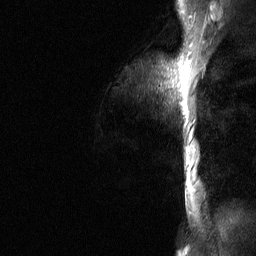
Breast MRI (dynamic contrast-enhanced), one sagittal slice; dynamic contrast-enhanced study with each time point stored as its own series, time point 2 of 3 at this slice position (early post-contrast, ordered by acquisition time); 1.5 T; TE 4.8 ms, TR 27 ms; 2 mm slice thickness; 256 × 256 image matrix, field of view 200 × 200 mm. Patient: female, 36 years. From the clinical record (not read from this slice): setting: breast cancer imaged before/during neoadjuvant chemotherapy; receptor status: HR-positive, HER2-negative.
Outlined on this slice (semi-automatically segmented with operator editing):
- analysis volume of interest (the breast-tissue region the enhancement analysis was run in; not a lesion): bounding box [x1, y1, x2, y2] px = [160, 54, 187, 210]
- tumour enhancement mask (voxels above the 90 % enhancement threshold inside the analysis volume of interest): [181, 61, 187, 115]